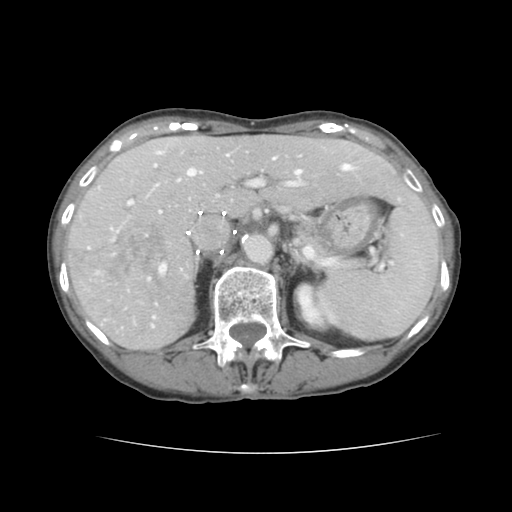
Contrast-enhanced abdominal CT, one axial slice. Position 91 of 136 along the scan axis. 120 kVp. Intravenous contrast given. Soft-tissue window (W 400 / L 40 HU). 2.5 mm slice thickness. 512 × 512 image matrix. Female patient, age 77 years. Case-level facts recorded for this patient, not image findings: diagnosis: colorectal cancer liver metastases, imaged before liver resection.
Structures marked on this image (outlined manually by an expert reader):
- hepatic veins: box from (x=151, y=152) to (x=352, y=327) px
- liver: (x=69, y=136)–(x=425, y=350)
- planned liver remnant (the part of the liver to remain after resection): (x=153, y=136)–(x=423, y=216)
- portal vein (with intrahepatic branches): (x=111, y=164)–(x=400, y=280)
- liver metastasis: (x=107, y=224)–(x=175, y=296)